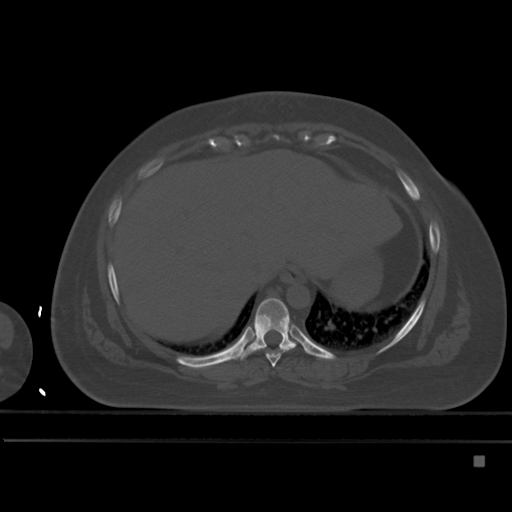
CT including the spine, one axial slice; slice 268 of 495 in the series (ordered by position); bone window (W 1800 / L 400 HU); 512 × 512 image matrix. Patient: female, 33 years. From the clinical record (not read from this slice): primary cancer: breast; vertebrae with lytic lesions (as recorded): T1.
Outlined on this slice (semi-automatically segmented with operator editing):
- T8 vertebra: bounding box (x1, y1, x2, y2) in pixels: (254, 348, 291, 367)
- T9 vertebra: (242, 298, 309, 360)